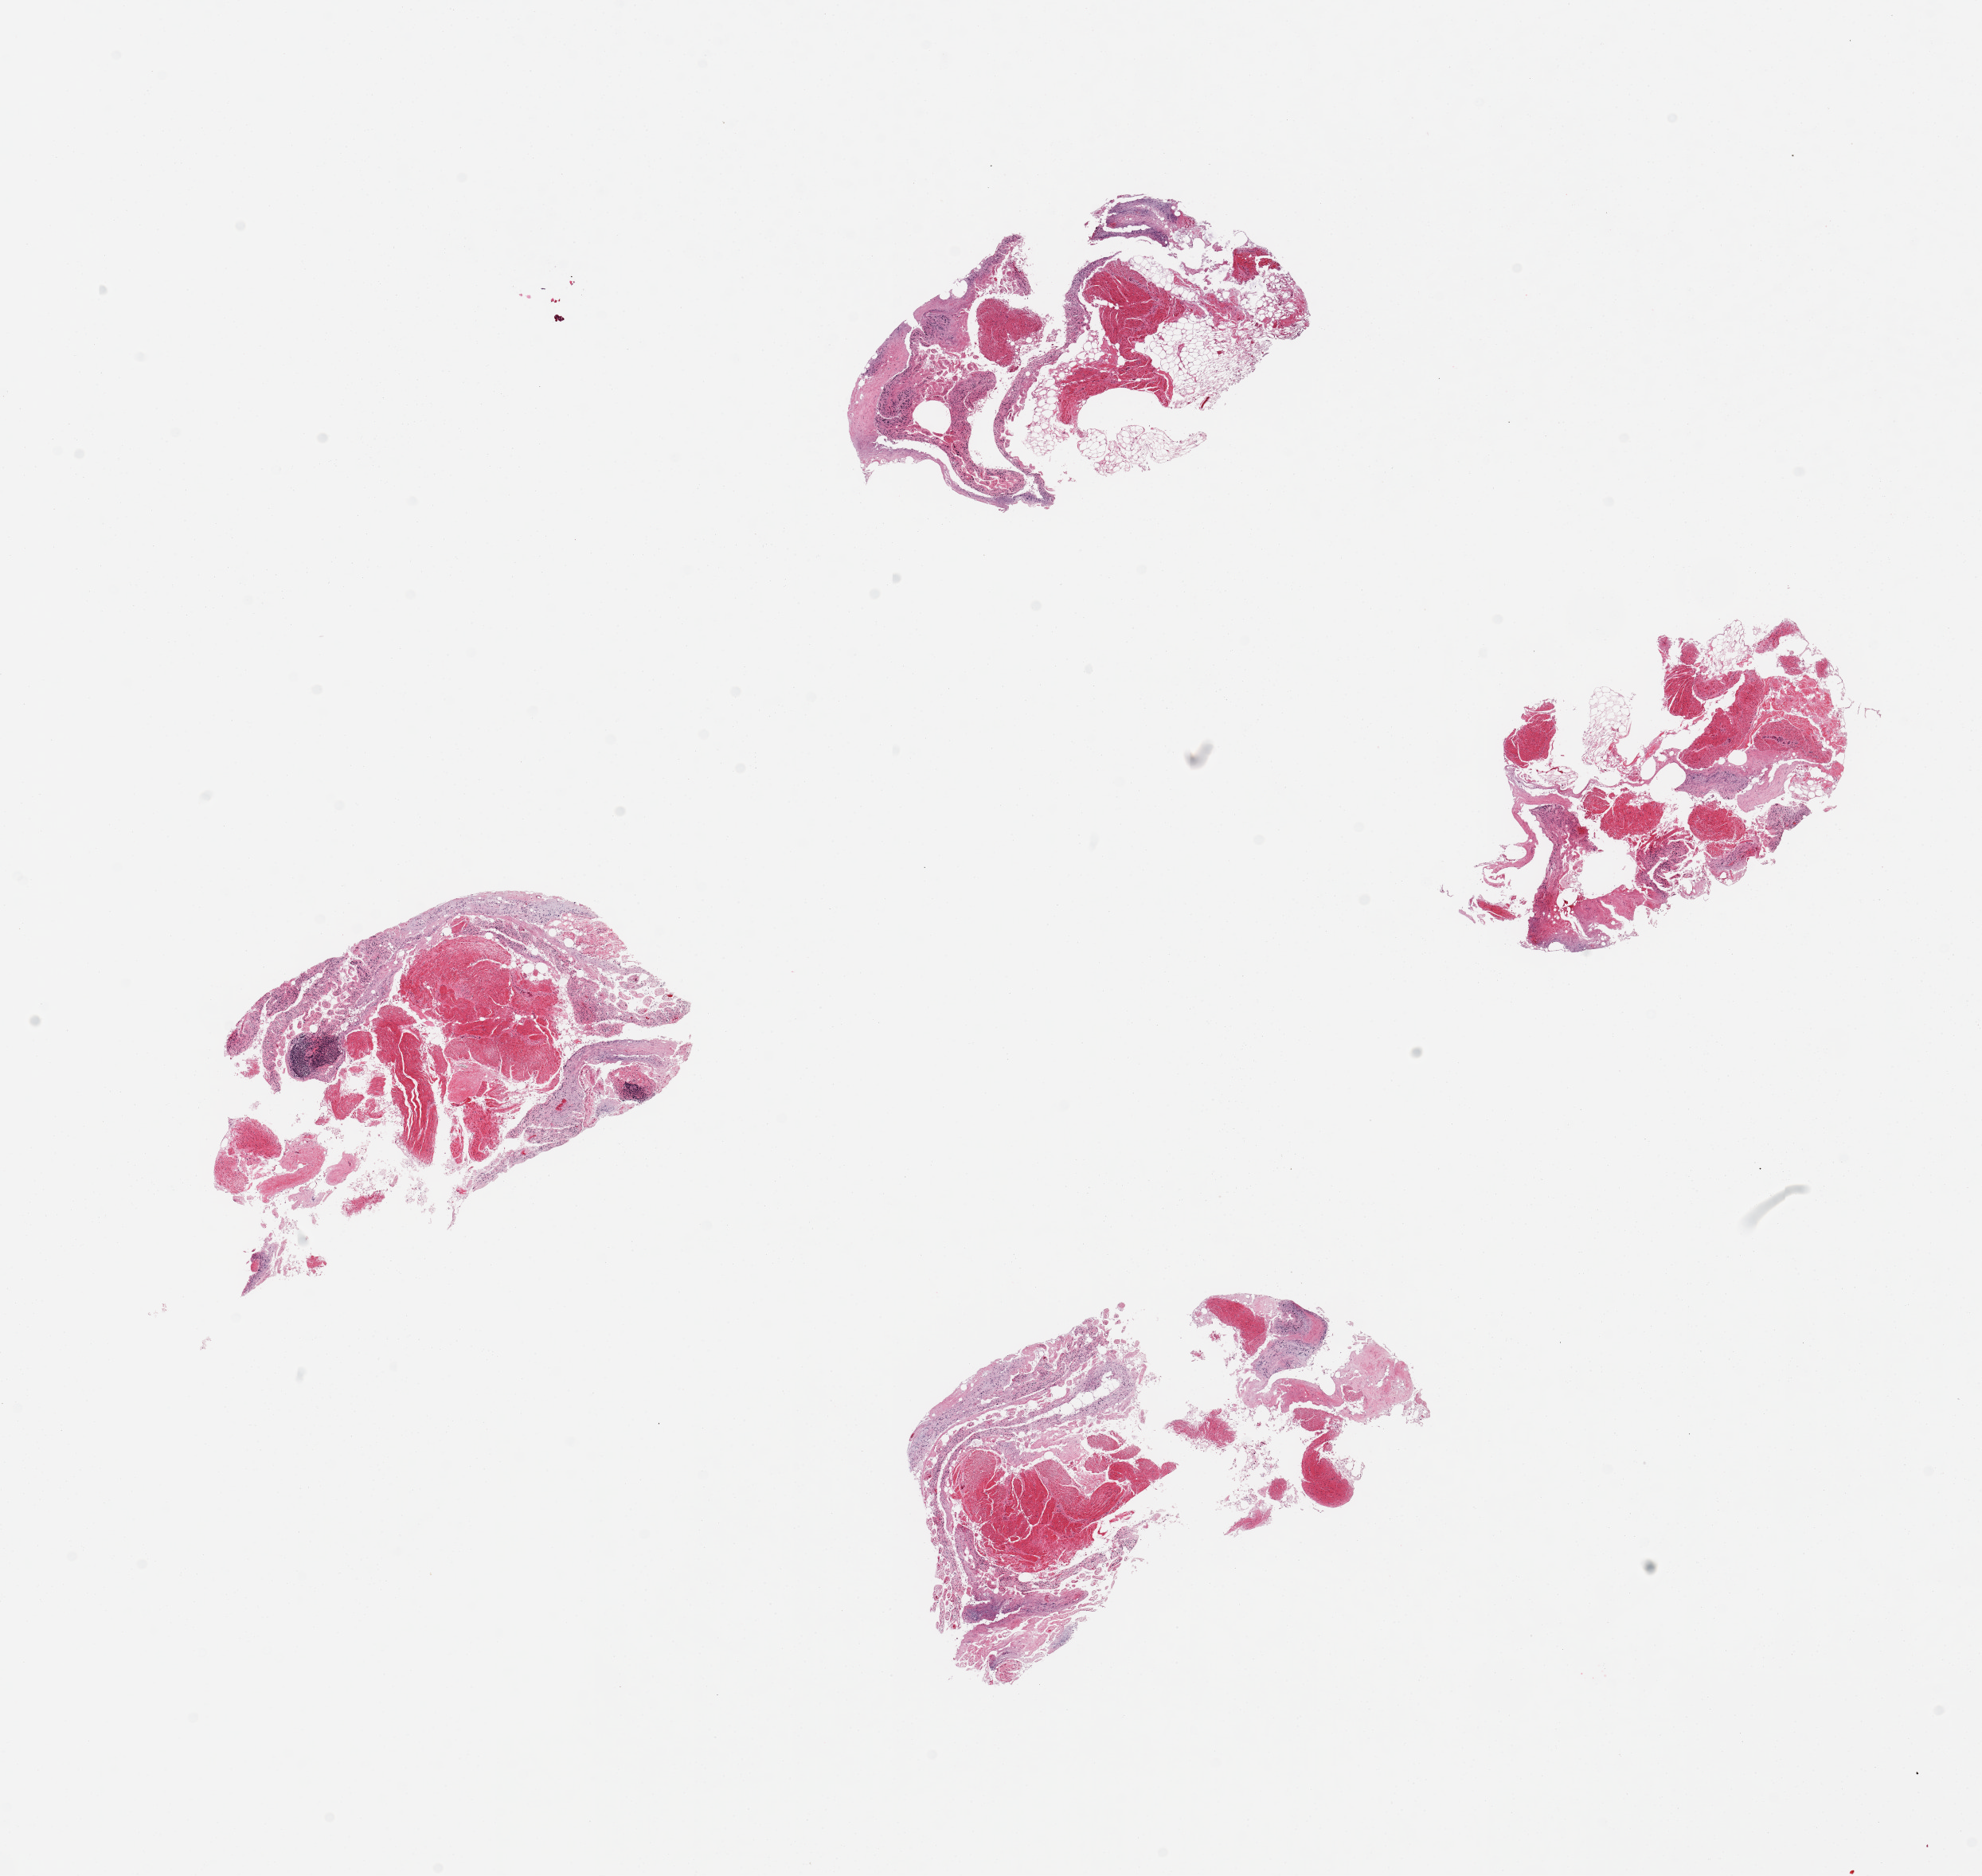
Whole-slide image, hematoxylin and eosin (H&E) stain, a low-resolution overview of the entire scanned area, about 19.7 x 18.6 mm. PAXgene-fixed, paraffin-embedded tissue. Sampled site (target tissue): ileum. Tissue donor sample. Male donor.
• review note (as recorded): 4 pieces; too autolyzed and with minimal lymphoid tissue